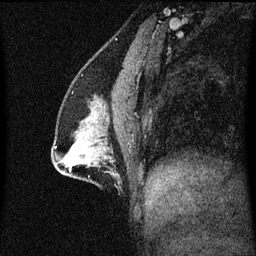
Breast MRI (dynamic contrast-enhanced), one sagittal slice. Slice 23 of 60 in the series (ordered by position). Dynamic contrast-enhanced series, image 2 of 3 at this slice position (ordered by acquisition). 1.5 T. TE 4.2 ms, TR 8.4 ms. 2 mm slice thickness. 256 × 256 image matrix, field of view 200 × 200 mm. Female patient, age 41 years. Case-level facts recorded for this patient, not image findings: setting: breast cancer imaged before/during neoadjuvant chemotherapy; receptor status: triple-negative.
Outlined on this slice (semi-automatic segmentation, software-assisted and operator-edited):
- analysis volume of interest (the breast-tissue region the enhancement analysis was run in; not a lesion): box from (x=52, y=104) to (x=125, y=175) px
- tumour enhancement mask (voxels above the 70 % enhancement threshold inside the analysis volume of interest): (x=72, y=146)–(x=77, y=149)